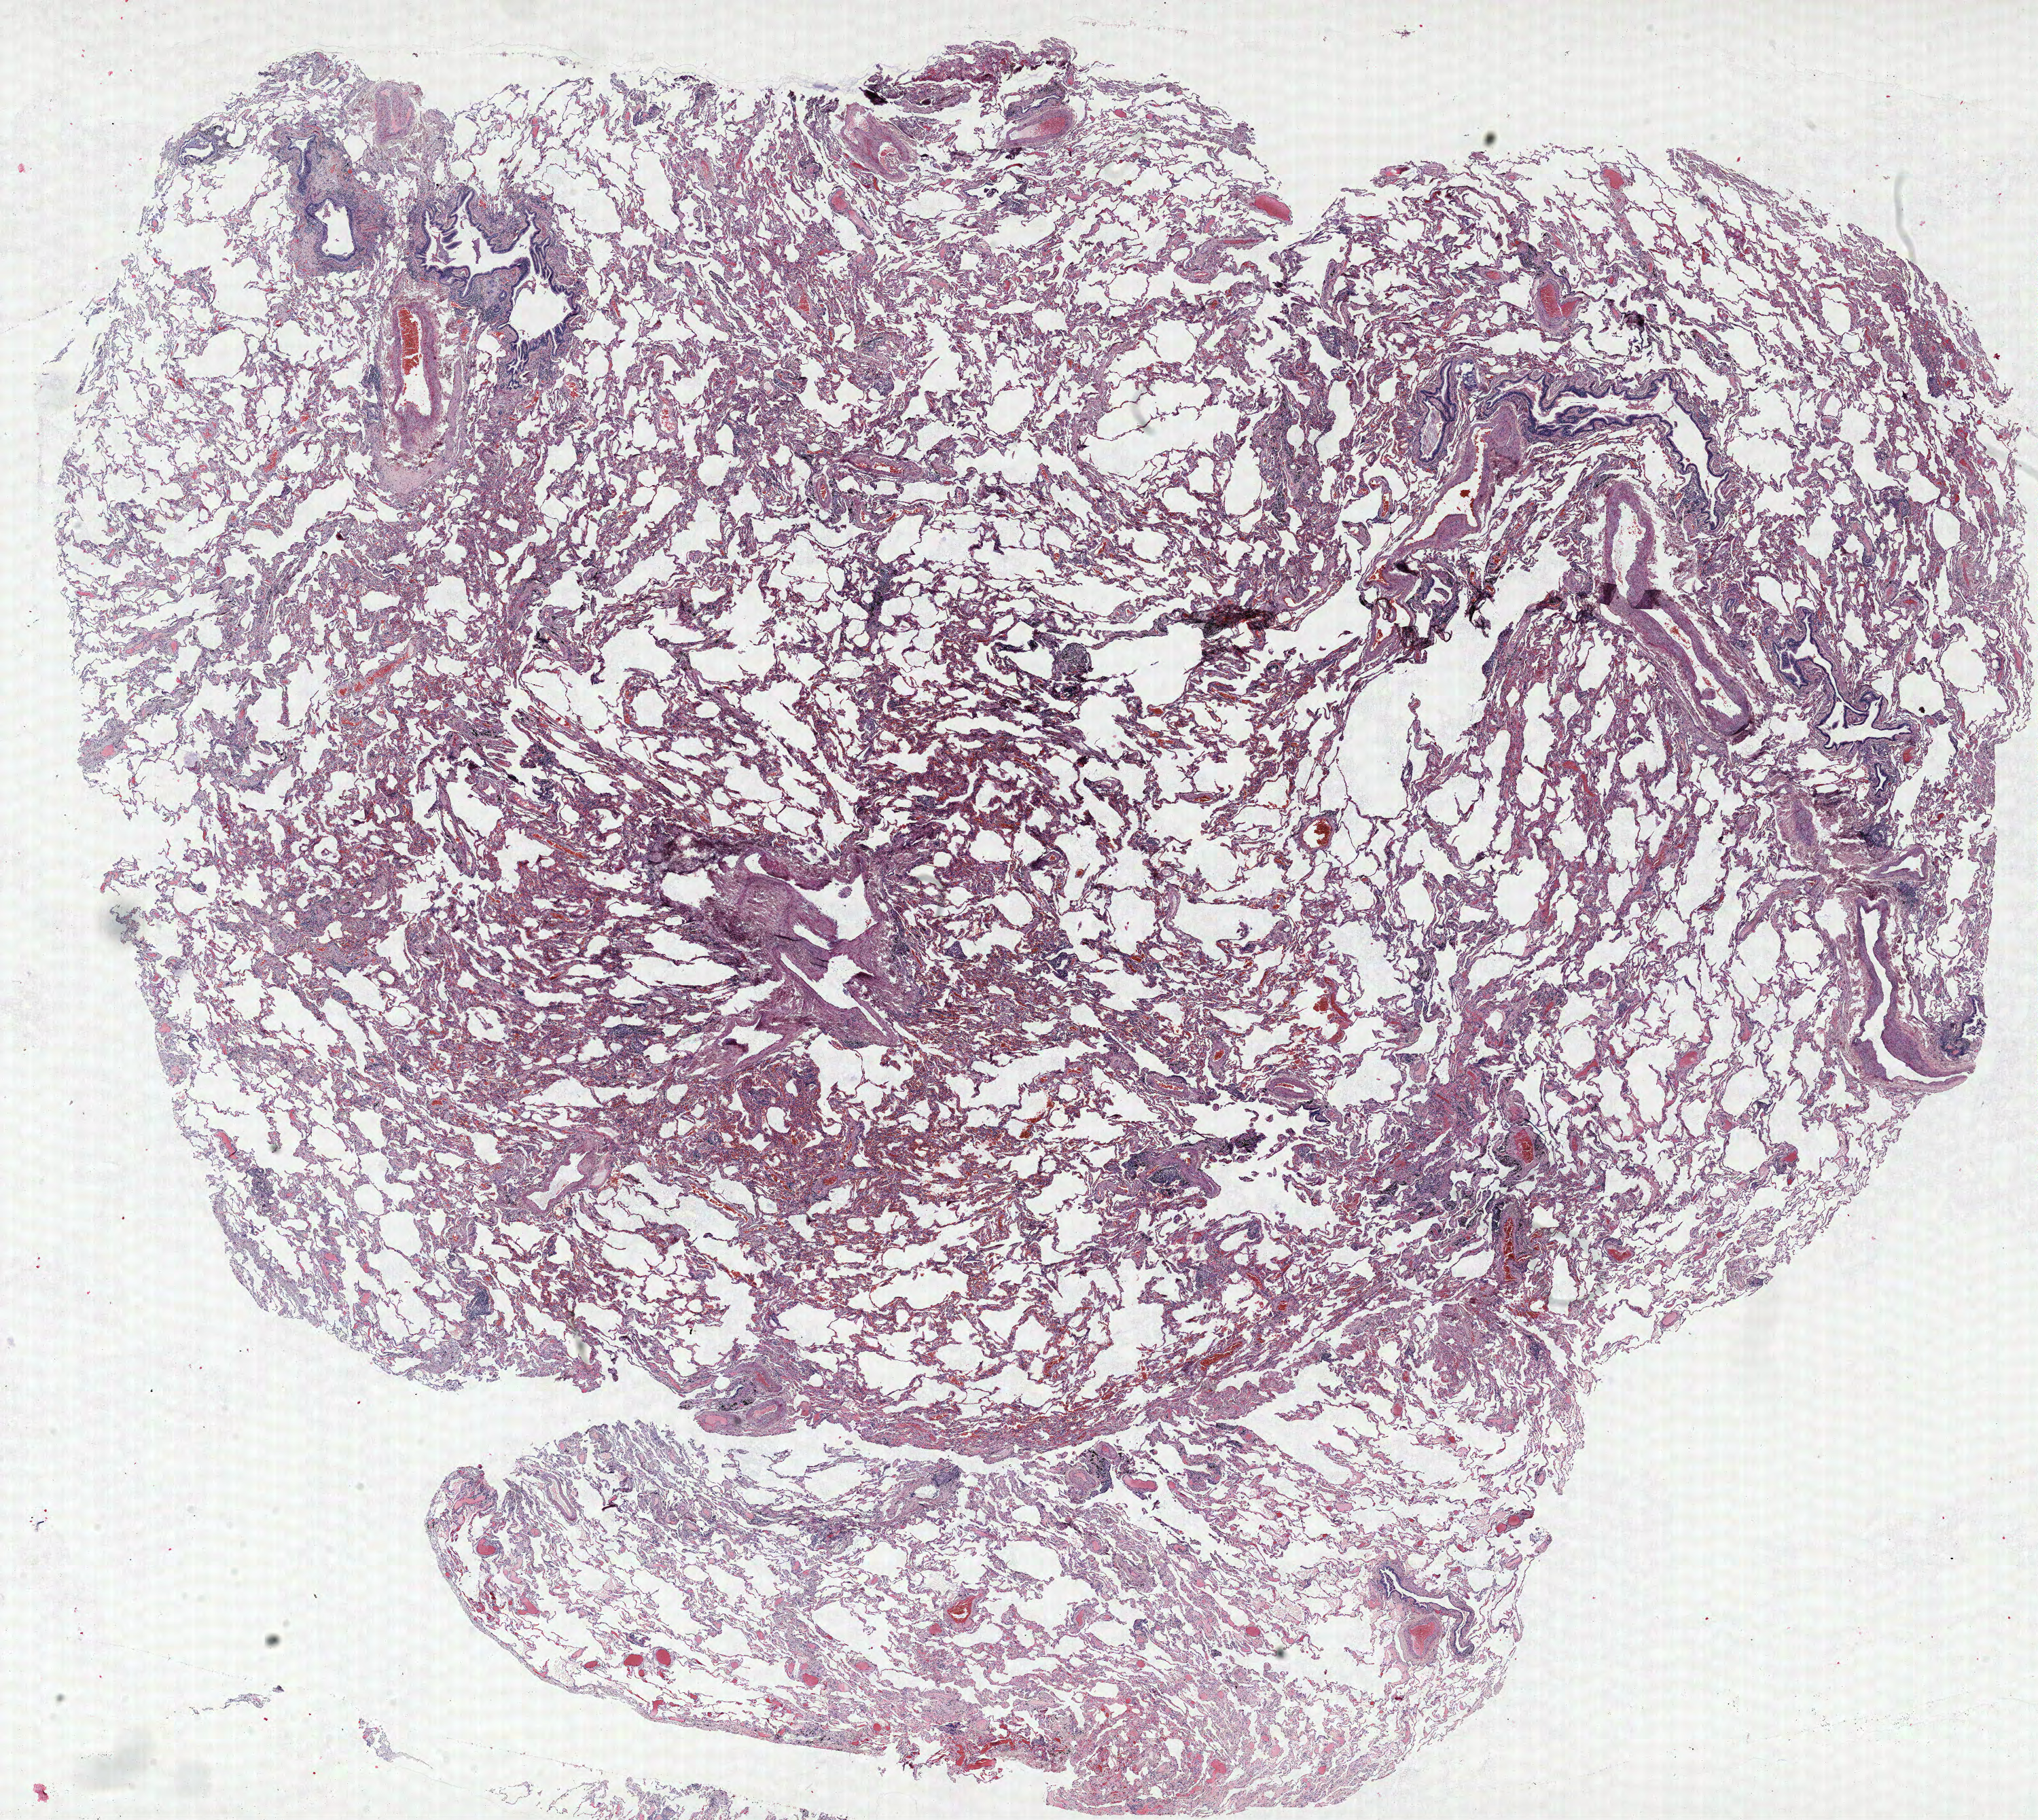
Whole-slide histology image, H&E-stained, a low-resolution overview of the entire scanned area, about 24.0 x 21.4 mm. FFPE section. Lung. Male, age 58 at enrolment. Former smoker at enrolment. Grade: poorly differentiated (G3).
• stage (AJCC 6th edition): IA
• ICD-O-3 topography: upper lobe of lung (C34.1)
• primary tumour location (clinical record): right upper lobe
• participant's lung-cancer diagnosis: Squamous cell carcinoma, NOS
• tumour size (pathology): 18 mm